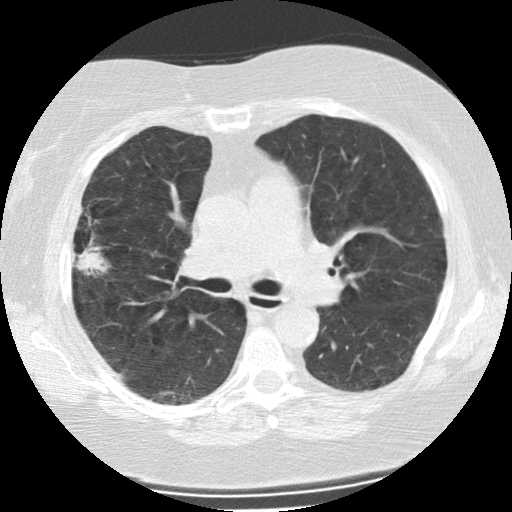
Low-dose screening chest CT, one axial slice; slice 141 of 225 in the series (ordered by position); reconstruction kernel STANDARD; lung window (W 1500 / L -600 HU); 512 × 512 image matrix.
Annotated regions visible in this slice (manually delineated by an expert):
- lesion 1 (tumor, upper lobe of right lung): bounding box (x1, y1, x2, y2) in pixels: (74, 242, 109, 275)